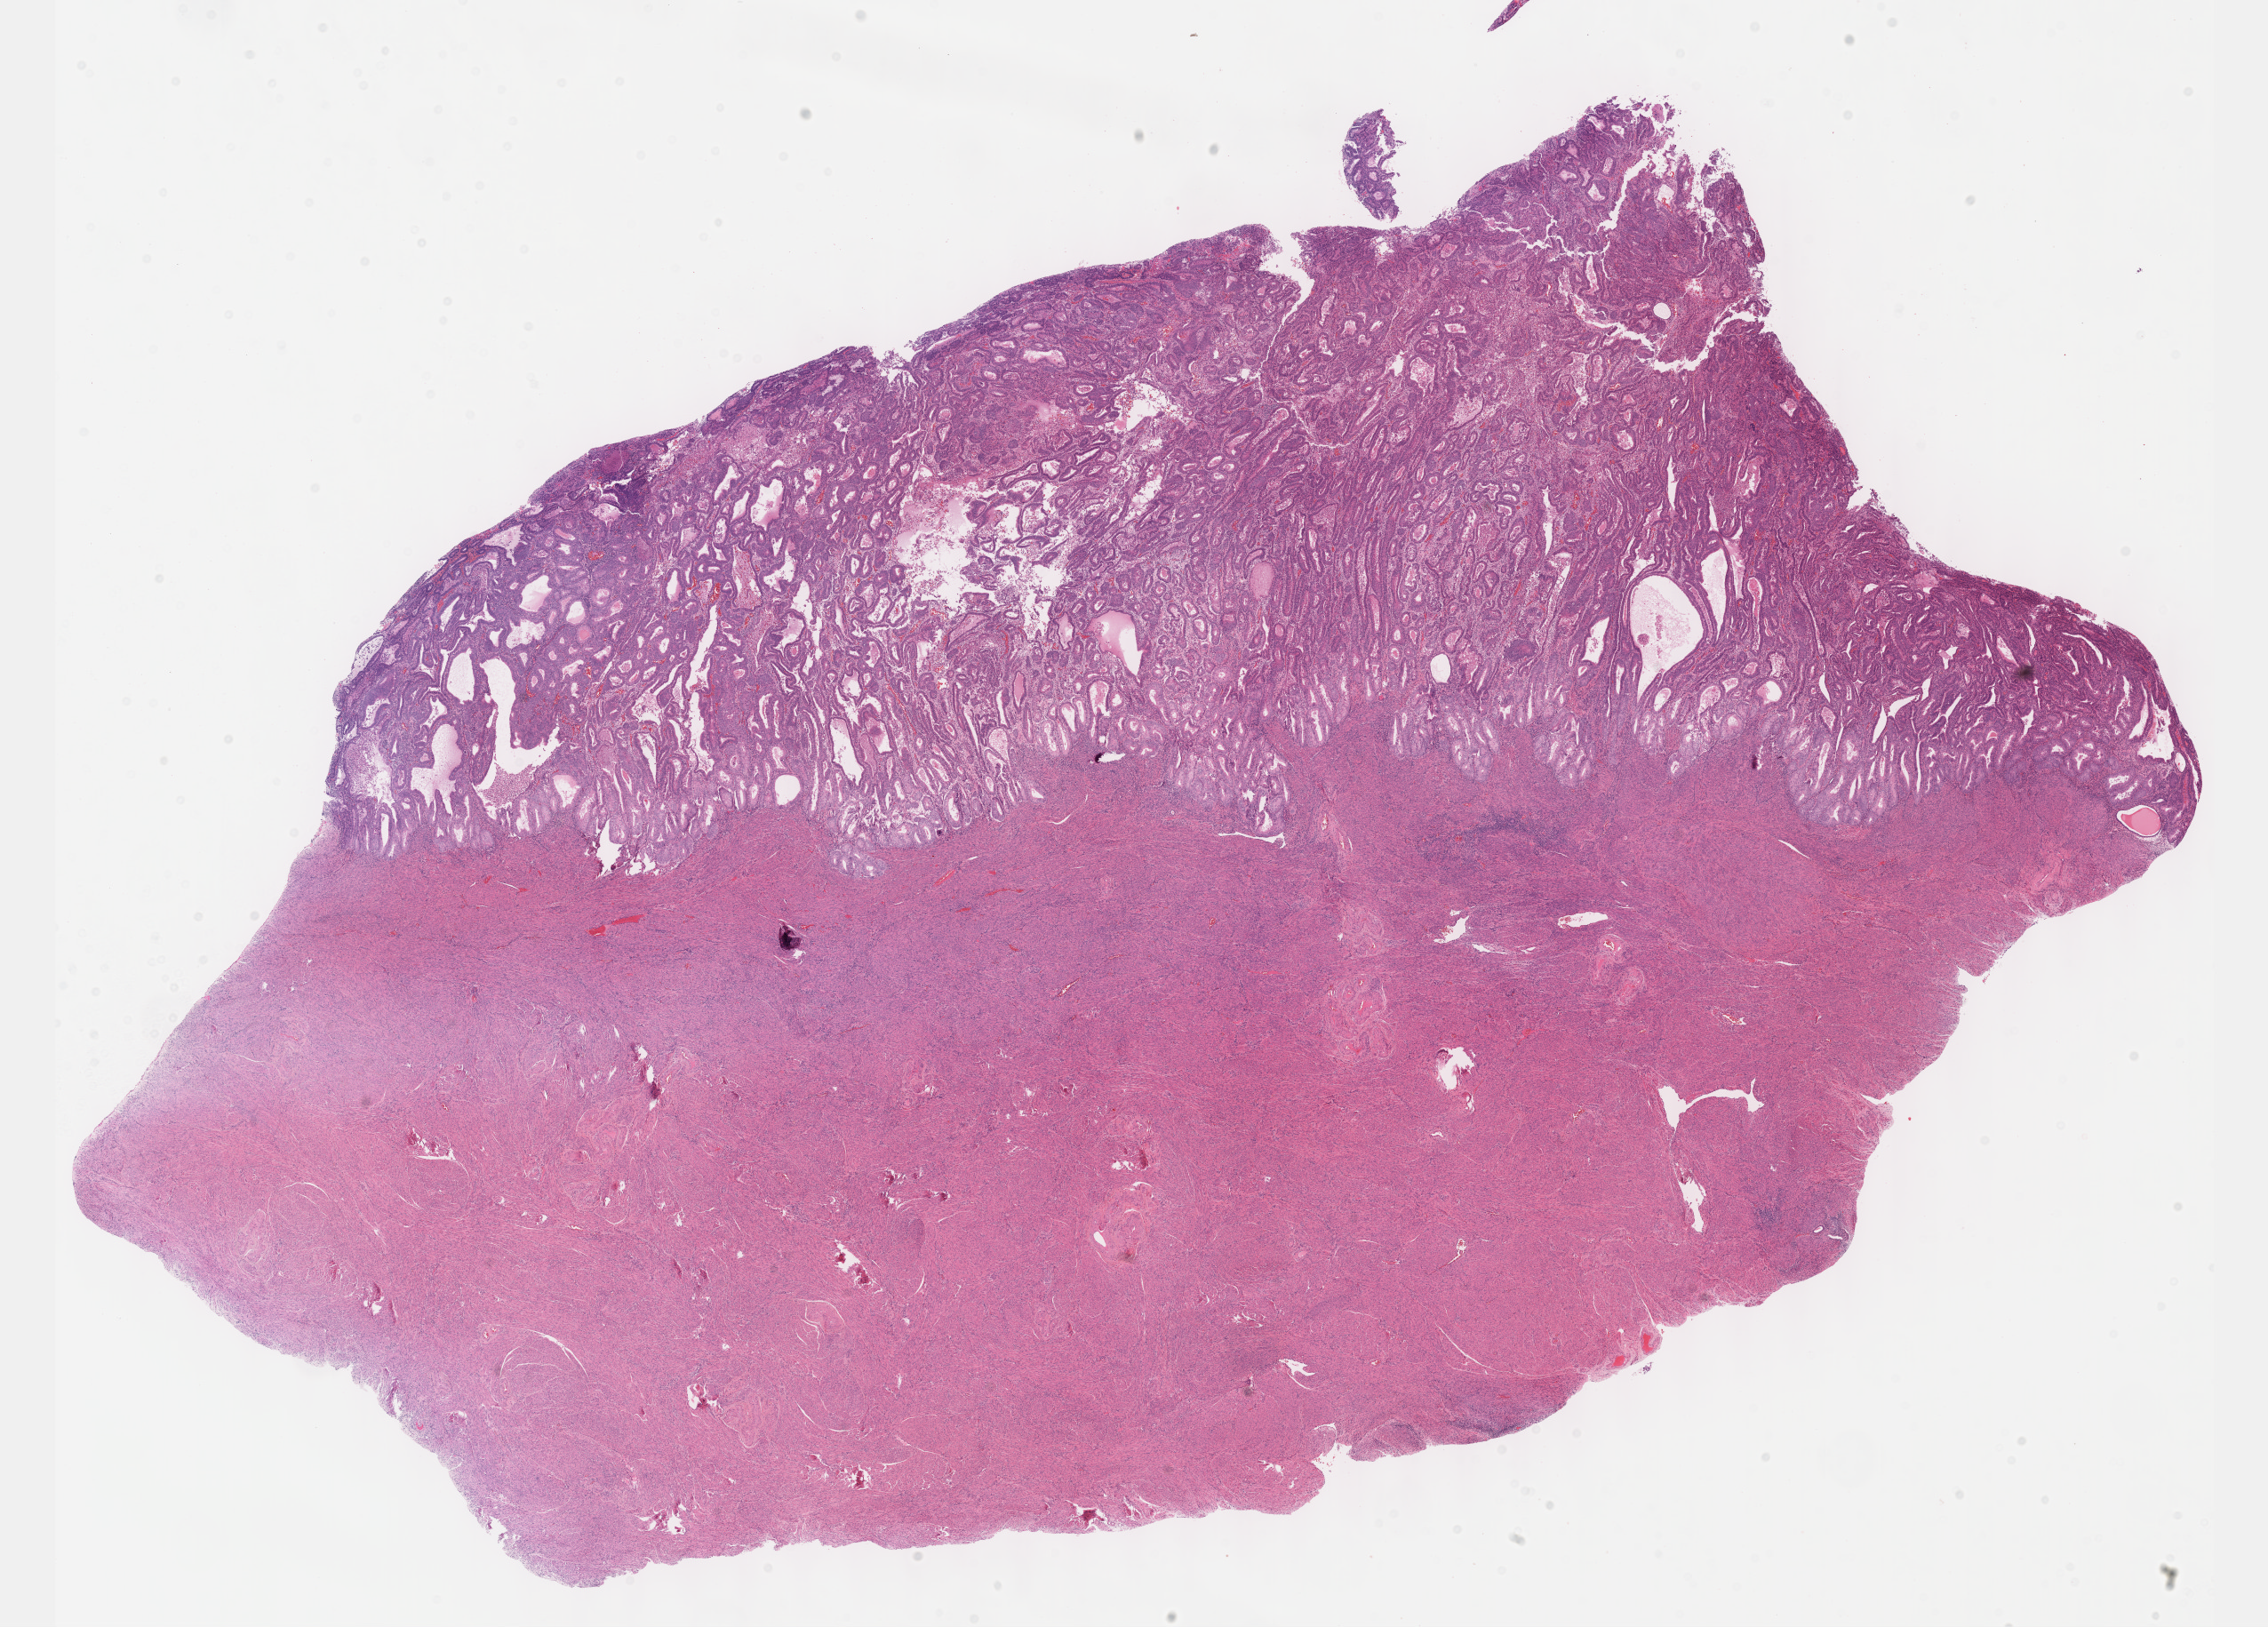
Whole-slide histology image, H&E, a low-resolution overview of the entire scanned area, about 20.6 x 14.8 mm, FFPE section, primary tumour sample from the uterus. Patient: female, age at initial diagnosis 70 years. Histologic grade: G2 (moderately differentiated).
* FIGO stage: I
* diagnosis: Endometrioid adenocarcinoma, NOS (endometrium)